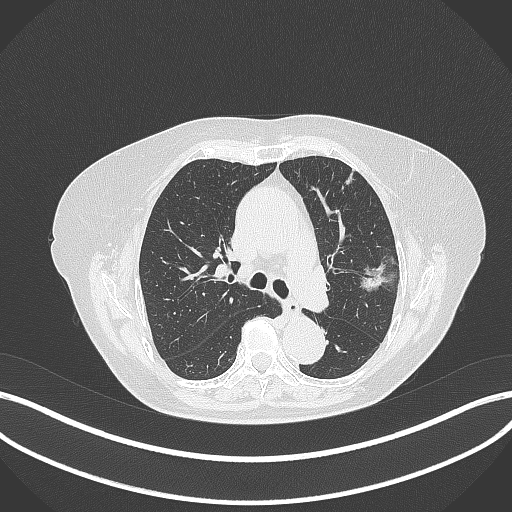
Chest CT, one axial slice; position 211 of 316 along the scan axis; 120 kVp; lung window (W 1500 / L -600 HU); 1 mm slice thickness; 512 × 512 image matrix, field of view 400 × 400 mm. Patient: female, 75 years. Case-level facts recorded for this patient, not image findings: clinical TNM (as recorded): T1c N0 M0.
Annotated regions visible in this slice (rectangle marked by the reading radiologist):
- lung tumour (recorded histology: adenocarcinoma): bounding box [x1, y1, x2, y2] px = [360, 258, 391, 296]